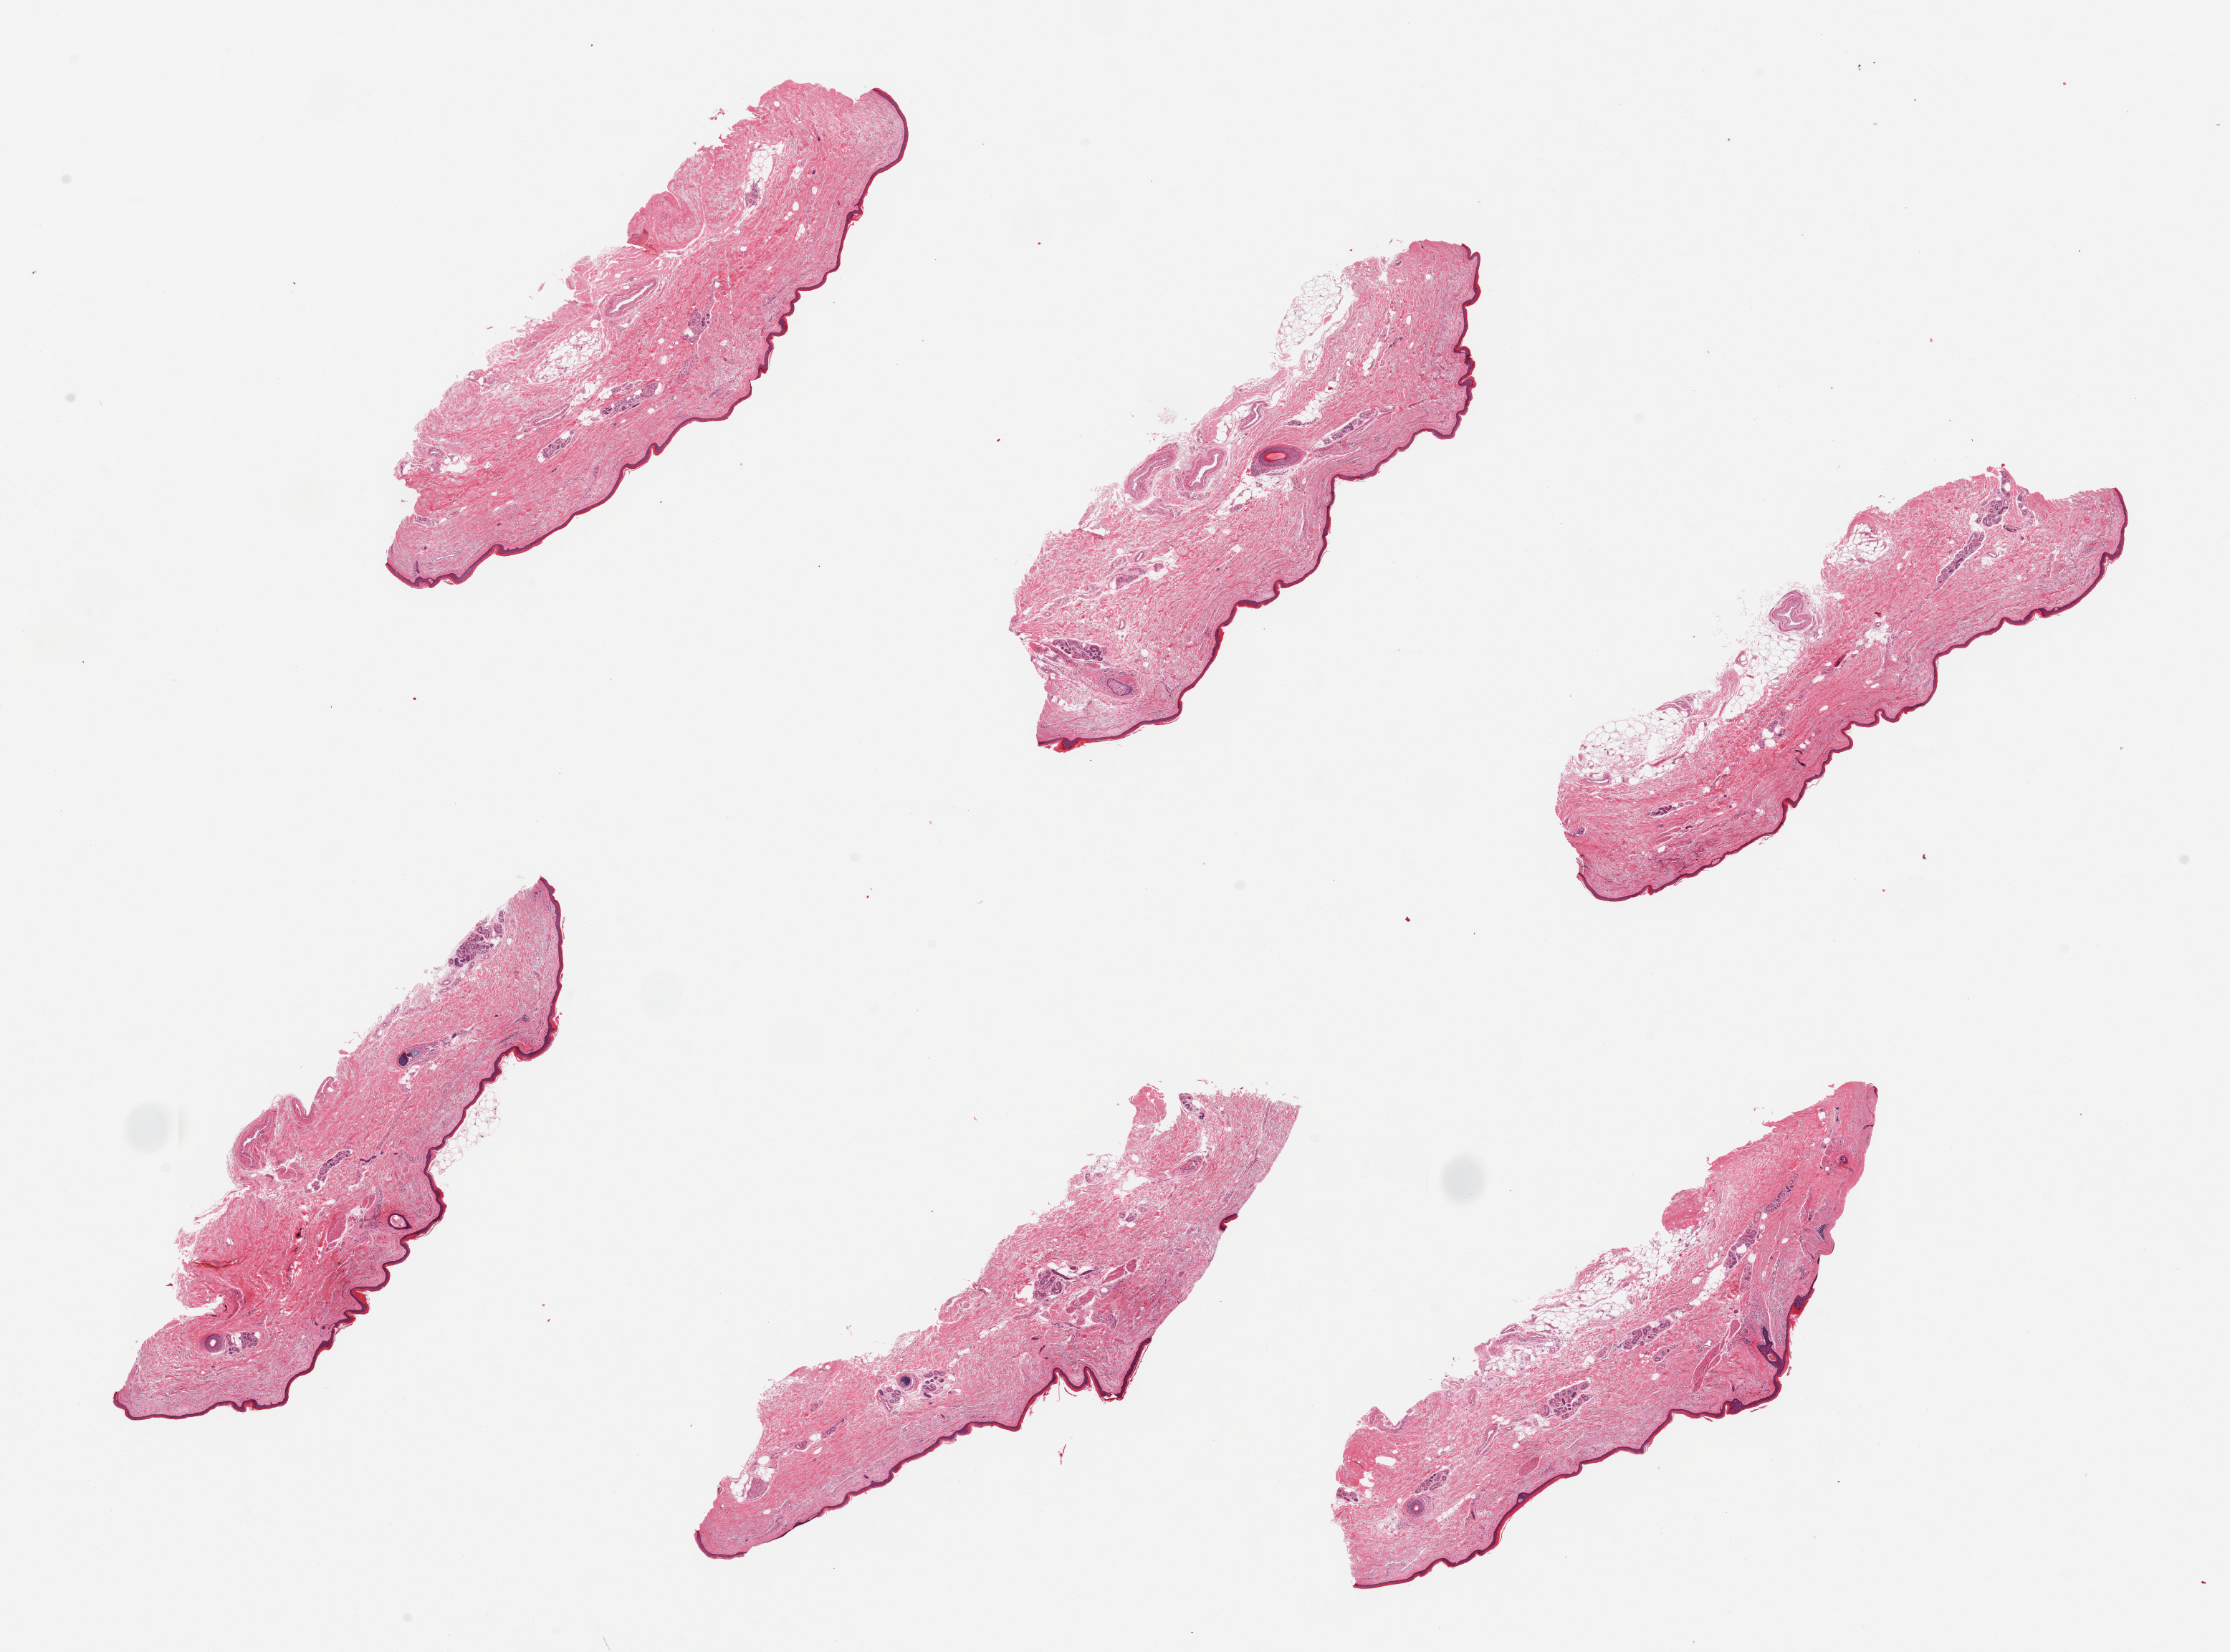
Whole-slide image, hematoxylin and eosin (H&E) stain, brightfield — low-resolution overview of the scanned area, about 24.6 x 18.2 mm (acquisition: 20x scan); PAXgene-fixed paraffin-embedded (PFPE) section; section of skin of lower leg (target tissue); donor tissue sample.
* pathologist's review note for this sample: 6 pieces, minimal dermal fat, squamous epithelium is ~40-60 microns